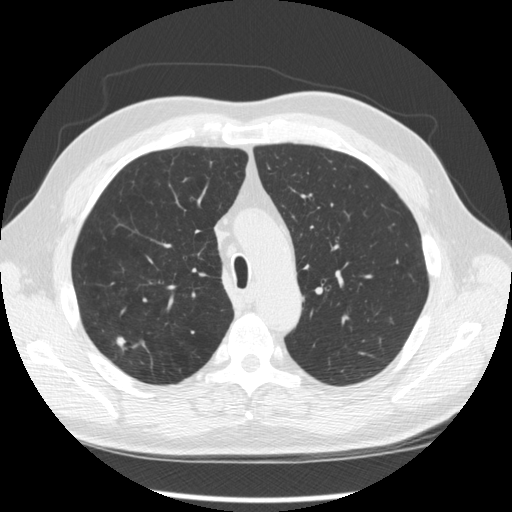
Low-dose screening chest CT, axial slice. Second screening round (one year after baseline). Lung window (W 1500 / L -600 HU). 2.5 mm slice thickness. Standard (soft-tissue) reconstruction kernel (STANDARD). Slice 78 of 289 in the series. 512 × 512 image matrix. Male participant, aged 64 years at enrolment. Former smoker at enrolment.
Lesion marked by an expert reader, bounding box (x1, y1, x2, y2) in pixels: (106, 325, 150, 366). The screening reader recorded 3 non-calcified nodules or masses ≥4 mm on this exam (right upper lobe, right upper lobe, right upper lobe); which of them this box marks is not recorded. Official screen result: positive, other. Lung cancer was diagnosed 411 days after this screen (after the third annual screen): adenocarcinoma, NOS, right upper lobe, moderately differentiated (G2), stage IA (AJCC 6th edition), 14 mm at pathology.